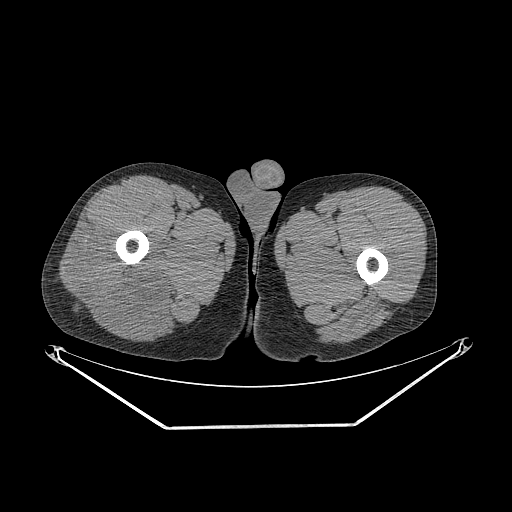
CT of an extremity soft-tissue mass (from a PET/CT study), one axial slice; reconstruction kernel STANDARD; 140 kVp; soft-tissue window (W 400 / L 40 HU); 3.75 mm slice thickness; 512 × 512 image matrix. Male patient. From the clinical record (not read from this slice): histological type: poorly differentiated synovial sarcoma; grade: high; site of the primary tumour: right buttock.
Structures marked on this image (expert contour drawn on MRI and transferred to this co-registered scan by the dataset authors):
- gross tumour volume including surrounding oedema: box from (x=59, y=226) to (x=177, y=334) px
- gross tumour volume (mass): (x=60, y=226)–(x=165, y=334)